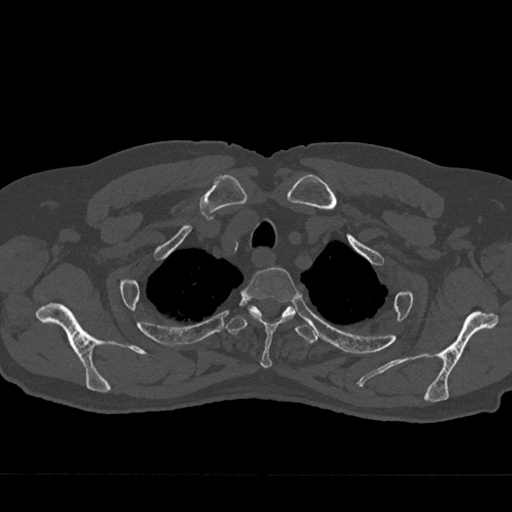
CT including the spine, one axial slice. Position 593 of 797 along the scan axis. Reconstruction kernel Br40s/3. Bone window (W 1800 / L 400 HU). 512 × 512 image matrix. Patient: male, 75 years. From the clinical record (not read from this slice): primary cancer: renal.
Outlined on this slice (semi-automatically segmented with operator editing):
- T2 vertebra: box from (x=242, y=267) to (x=299, y=368) px
- T3 vertebra: (x=226, y=306)–(x=318, y=344)